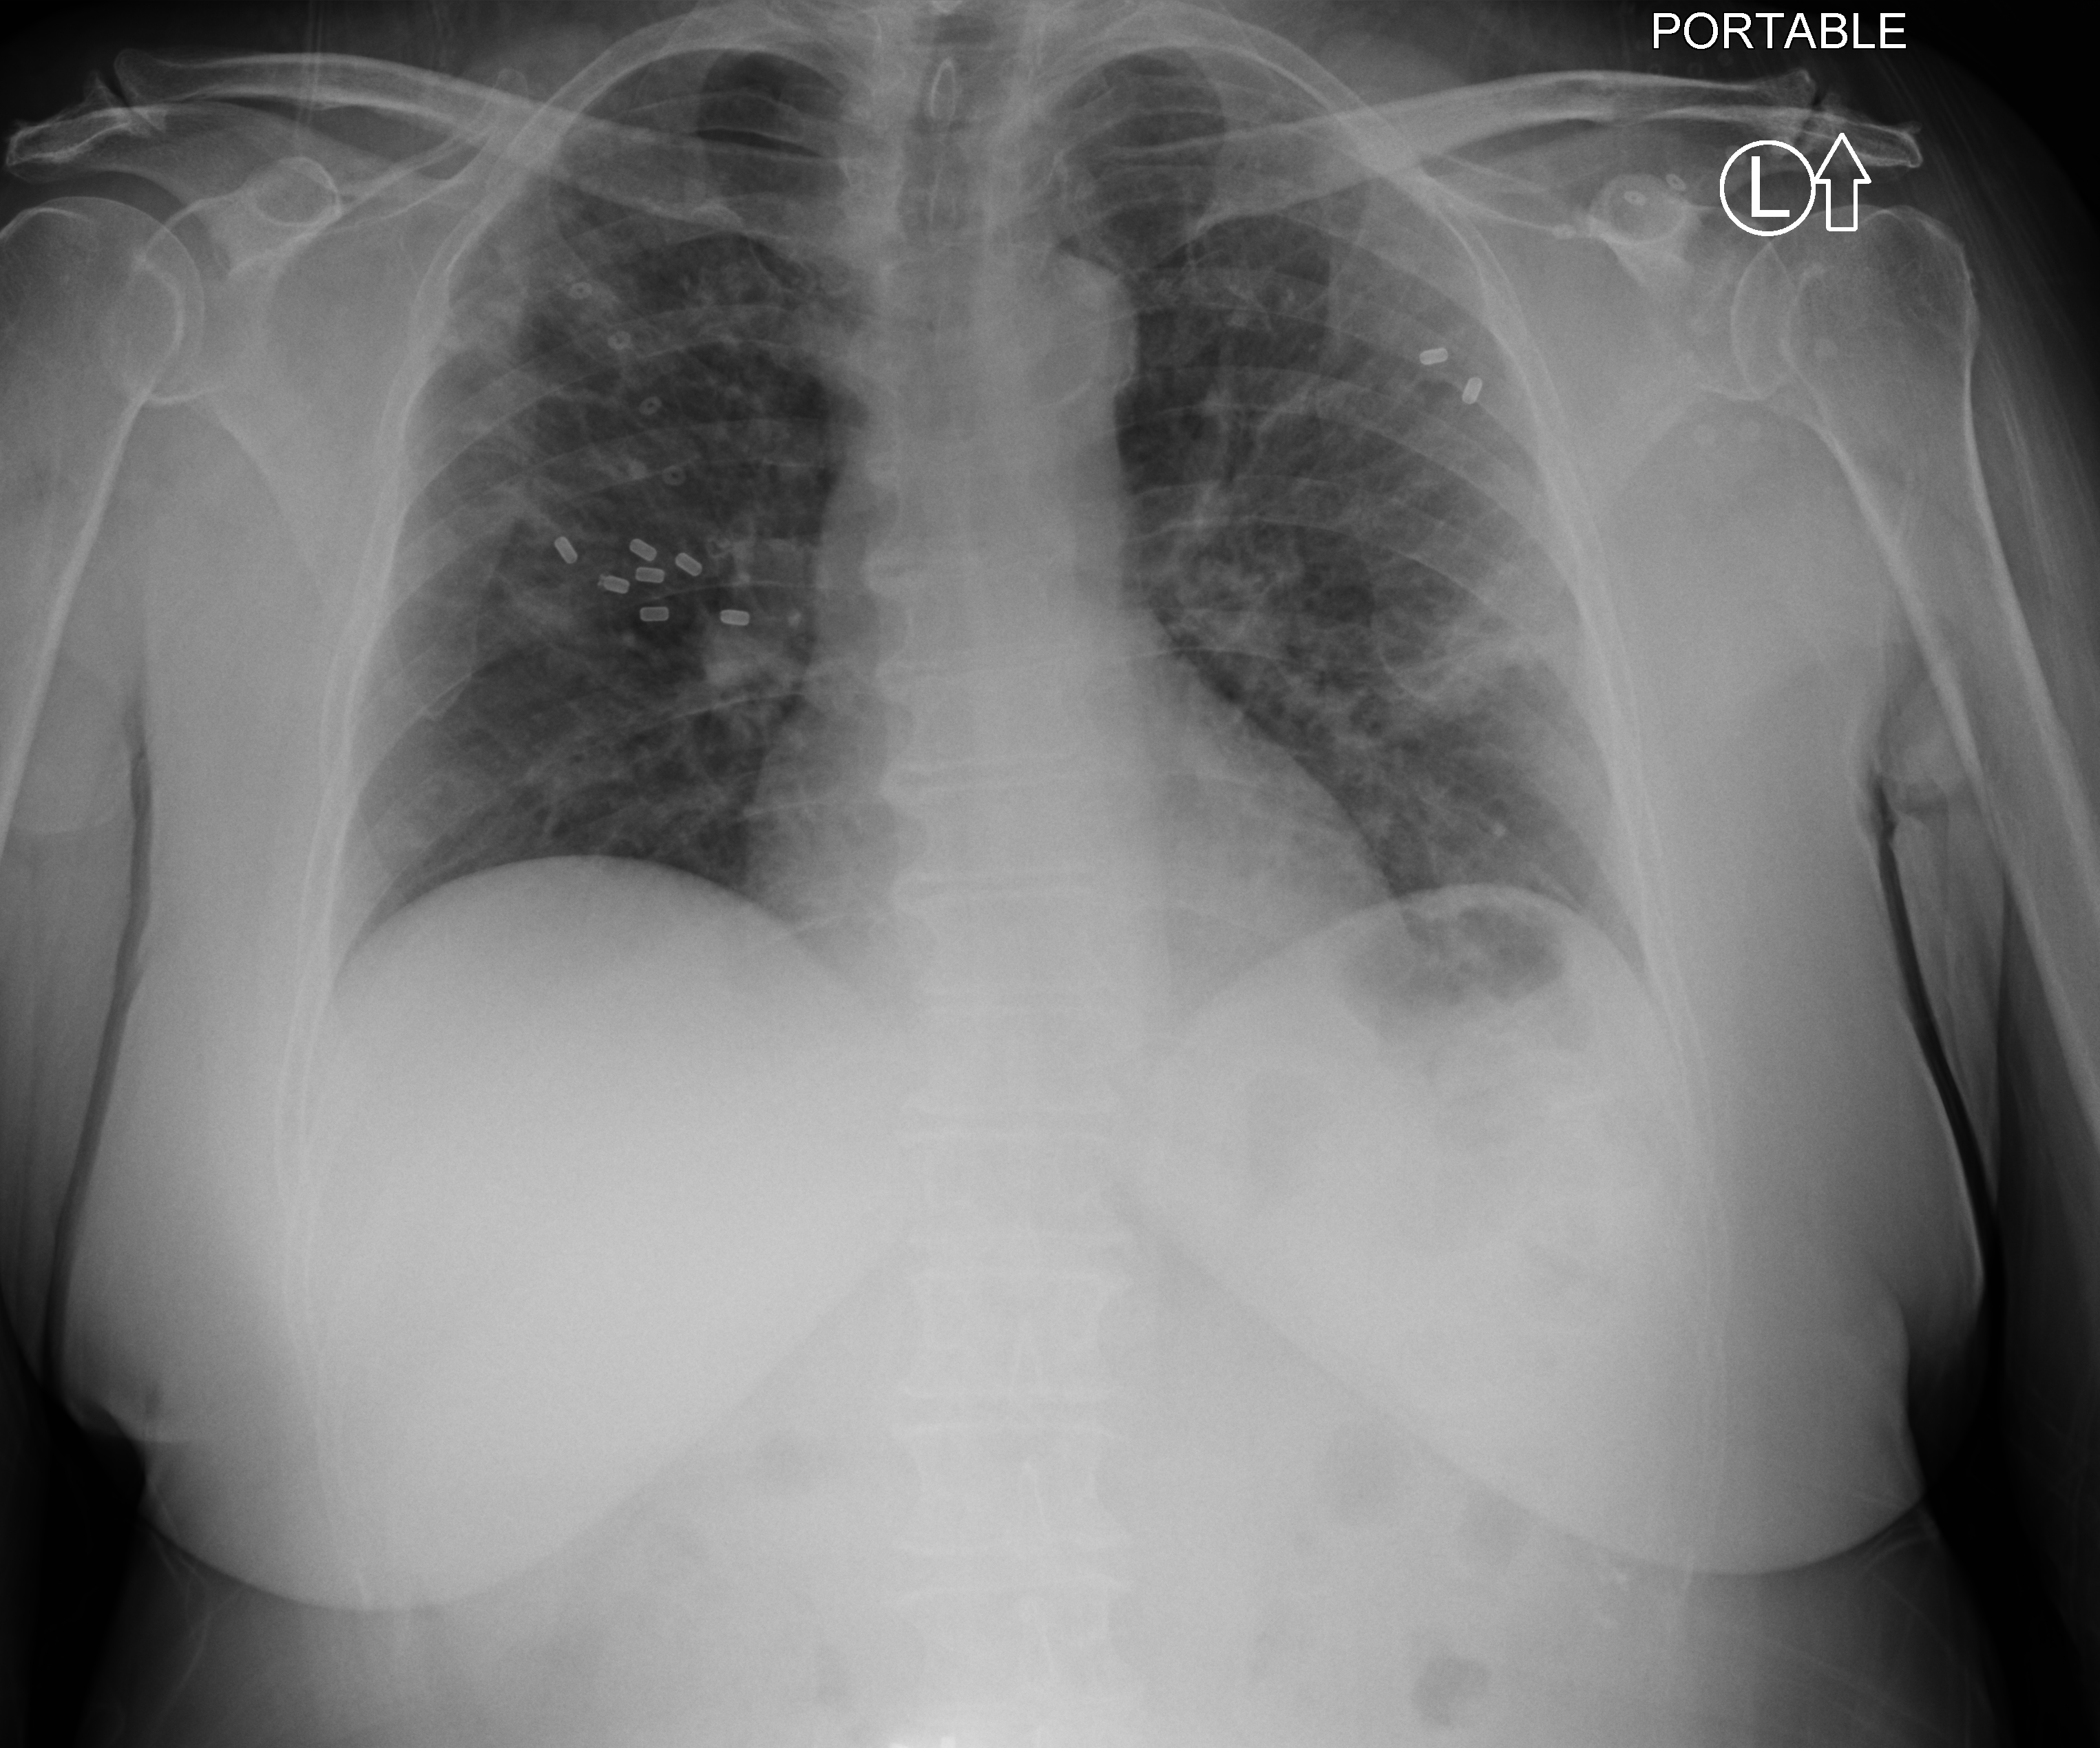
Chest X-ray (portable); anteroposterior (AP) projection. Female patient hospitalised with COVID-19, age 60–74 years.
Admission-level facts for this patient (not findings on this image; timing relative to this image not recorded):
- other chronic lung disease (admission record): no
- length of hospital stay: 4 days